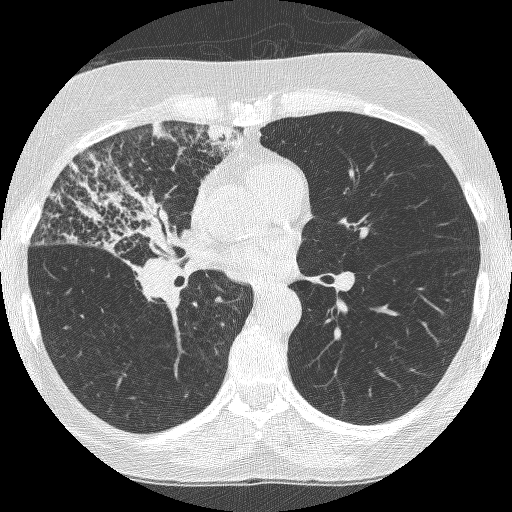
Axial slice from a low-dose chest CT screening exam; third screening round (two years after baseline); lung window (W 1500 / L -600 HU); lung (sharp) reconstruction kernel (BONE); slice 137 of 253 in the series; 512 × 512 image matrix. Female participant, aged 64 years at enrolment.
Lesion marked by an expert reader, bounding box (x1, y1, x2, y2) in pixels: (59, 168, 200, 311). Screening reader's record for this exam (one nodule recorded; not confirmed to be the boxed lesion): non-calcified nodule or mass ≥4 mm, right upper lobe, 49 × 43 mm, spiculated (stellate) margins, soft tissue attenuation, pre-existing on the prior screen: yes; interval growth: yes. Official screen result: positive, other. Later outcome: lung cancer diagnosed 7 days after this screen — adenocarcinoma, NOS, right upper lobe, right middle lobe, right hilum, stage IV (AJCC 6th edition), 85 mm at pathology.